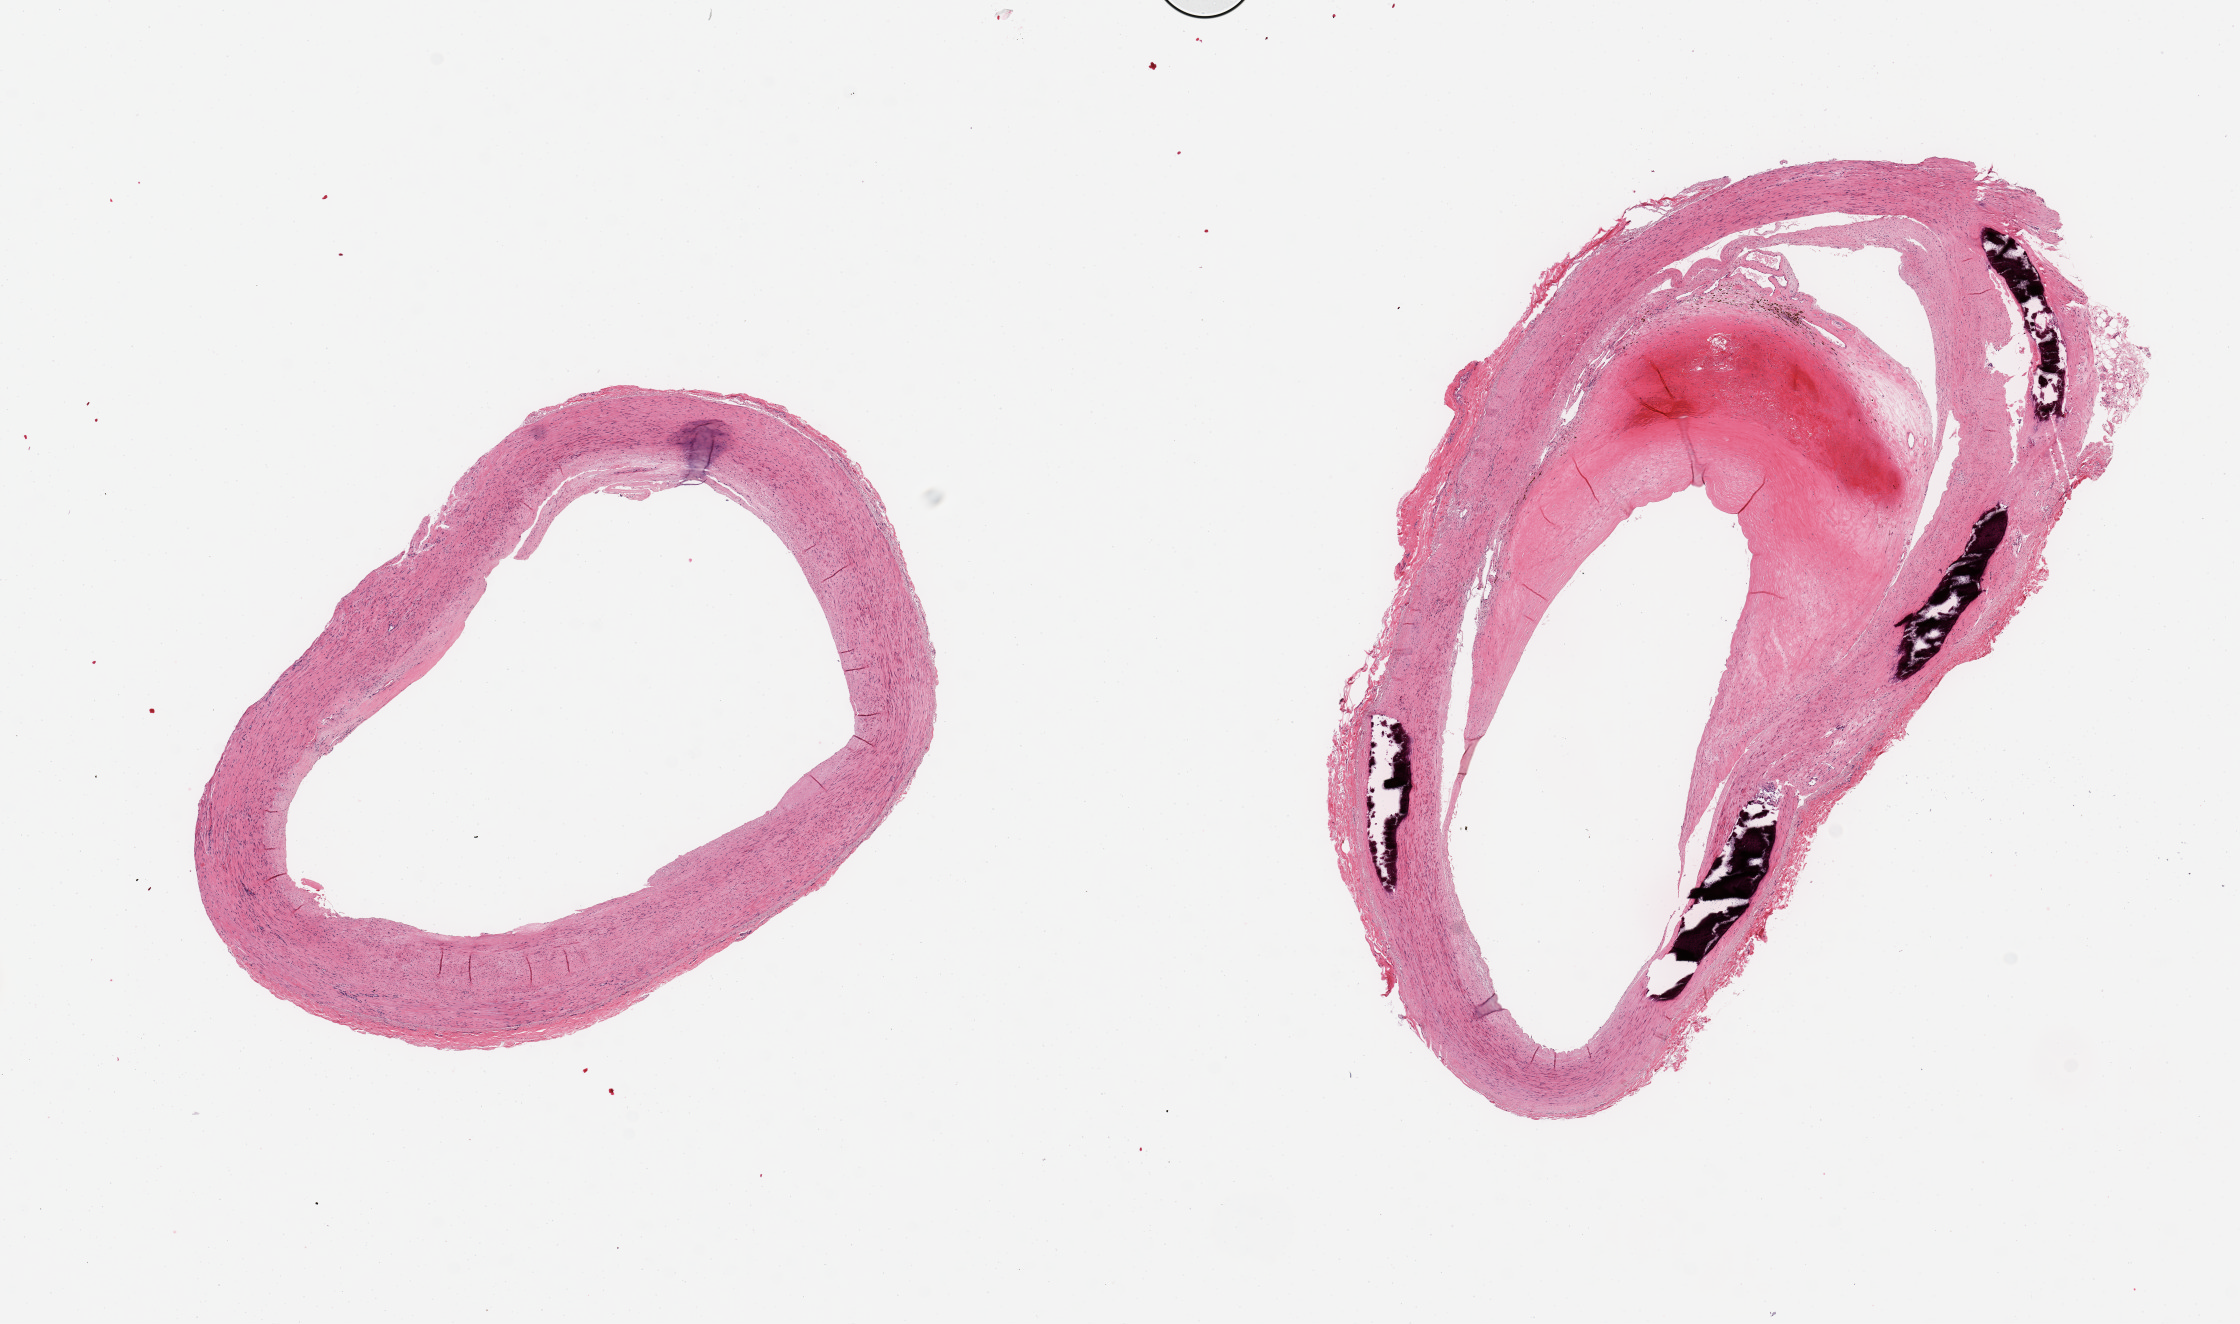
Digitized hematoxylin and eosin (H&E)-stained section — a low-resolution overview of the entire scanned area, about 17.7 x 10.5 mm; PAXgene-fixed paraffin-embedded (PFPE) section; target tissue: tibial artery; donor tissue sample. Donor: male.
- reviewer comment on this tissue sample: 2 pieces, prominent Mockeberg medial sclerosis, ~40% atherotic occlusion